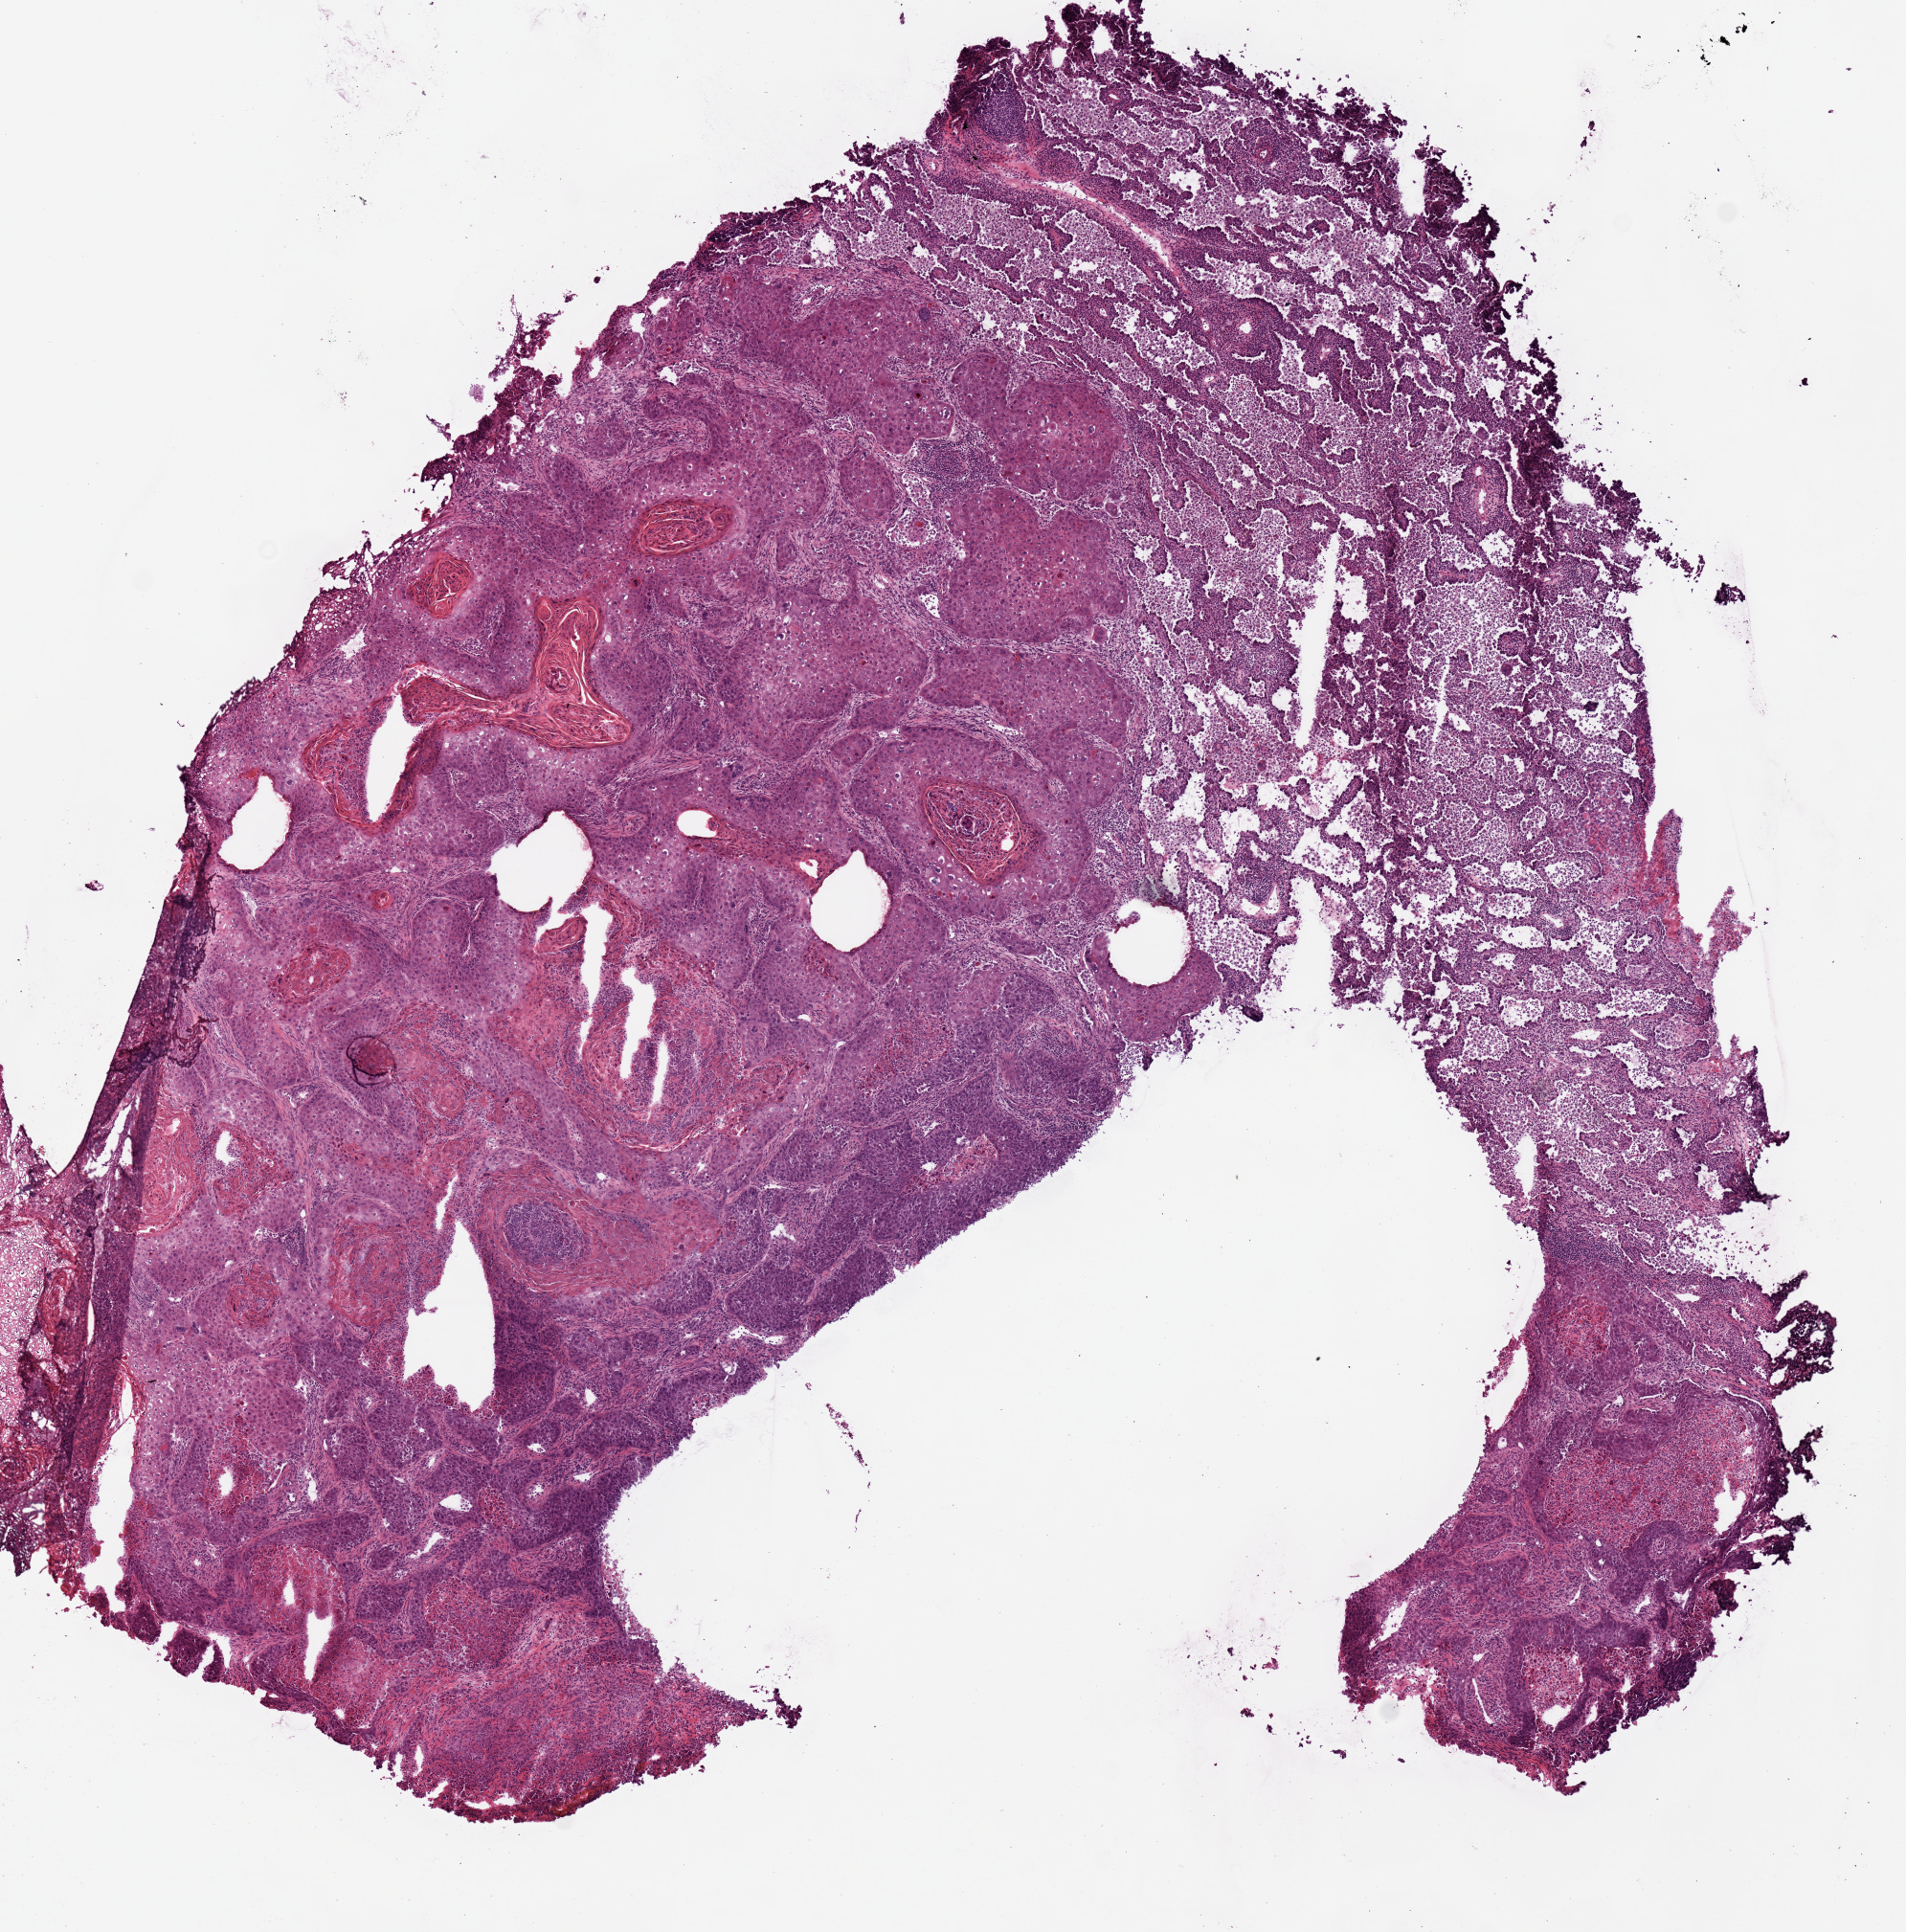
Whole-slide histology image, H&E, low-resolution overview of the scanned area, about 7.9 x 8.0 mm; frozen section; primary tumour sample from the lung. Patient: male, age at initial diagnosis 67 years. Pathologist review of this section (percent, as recorded): tumour cells 90%, tumour nuclei 70%, normal cells 0%, stromal cells 10%, necrosis 0%.
Histologic diagnosis: Squamous cell carcinoma, NOS. Laterality: left. AJCC pathologic stage: IB (6th edition).